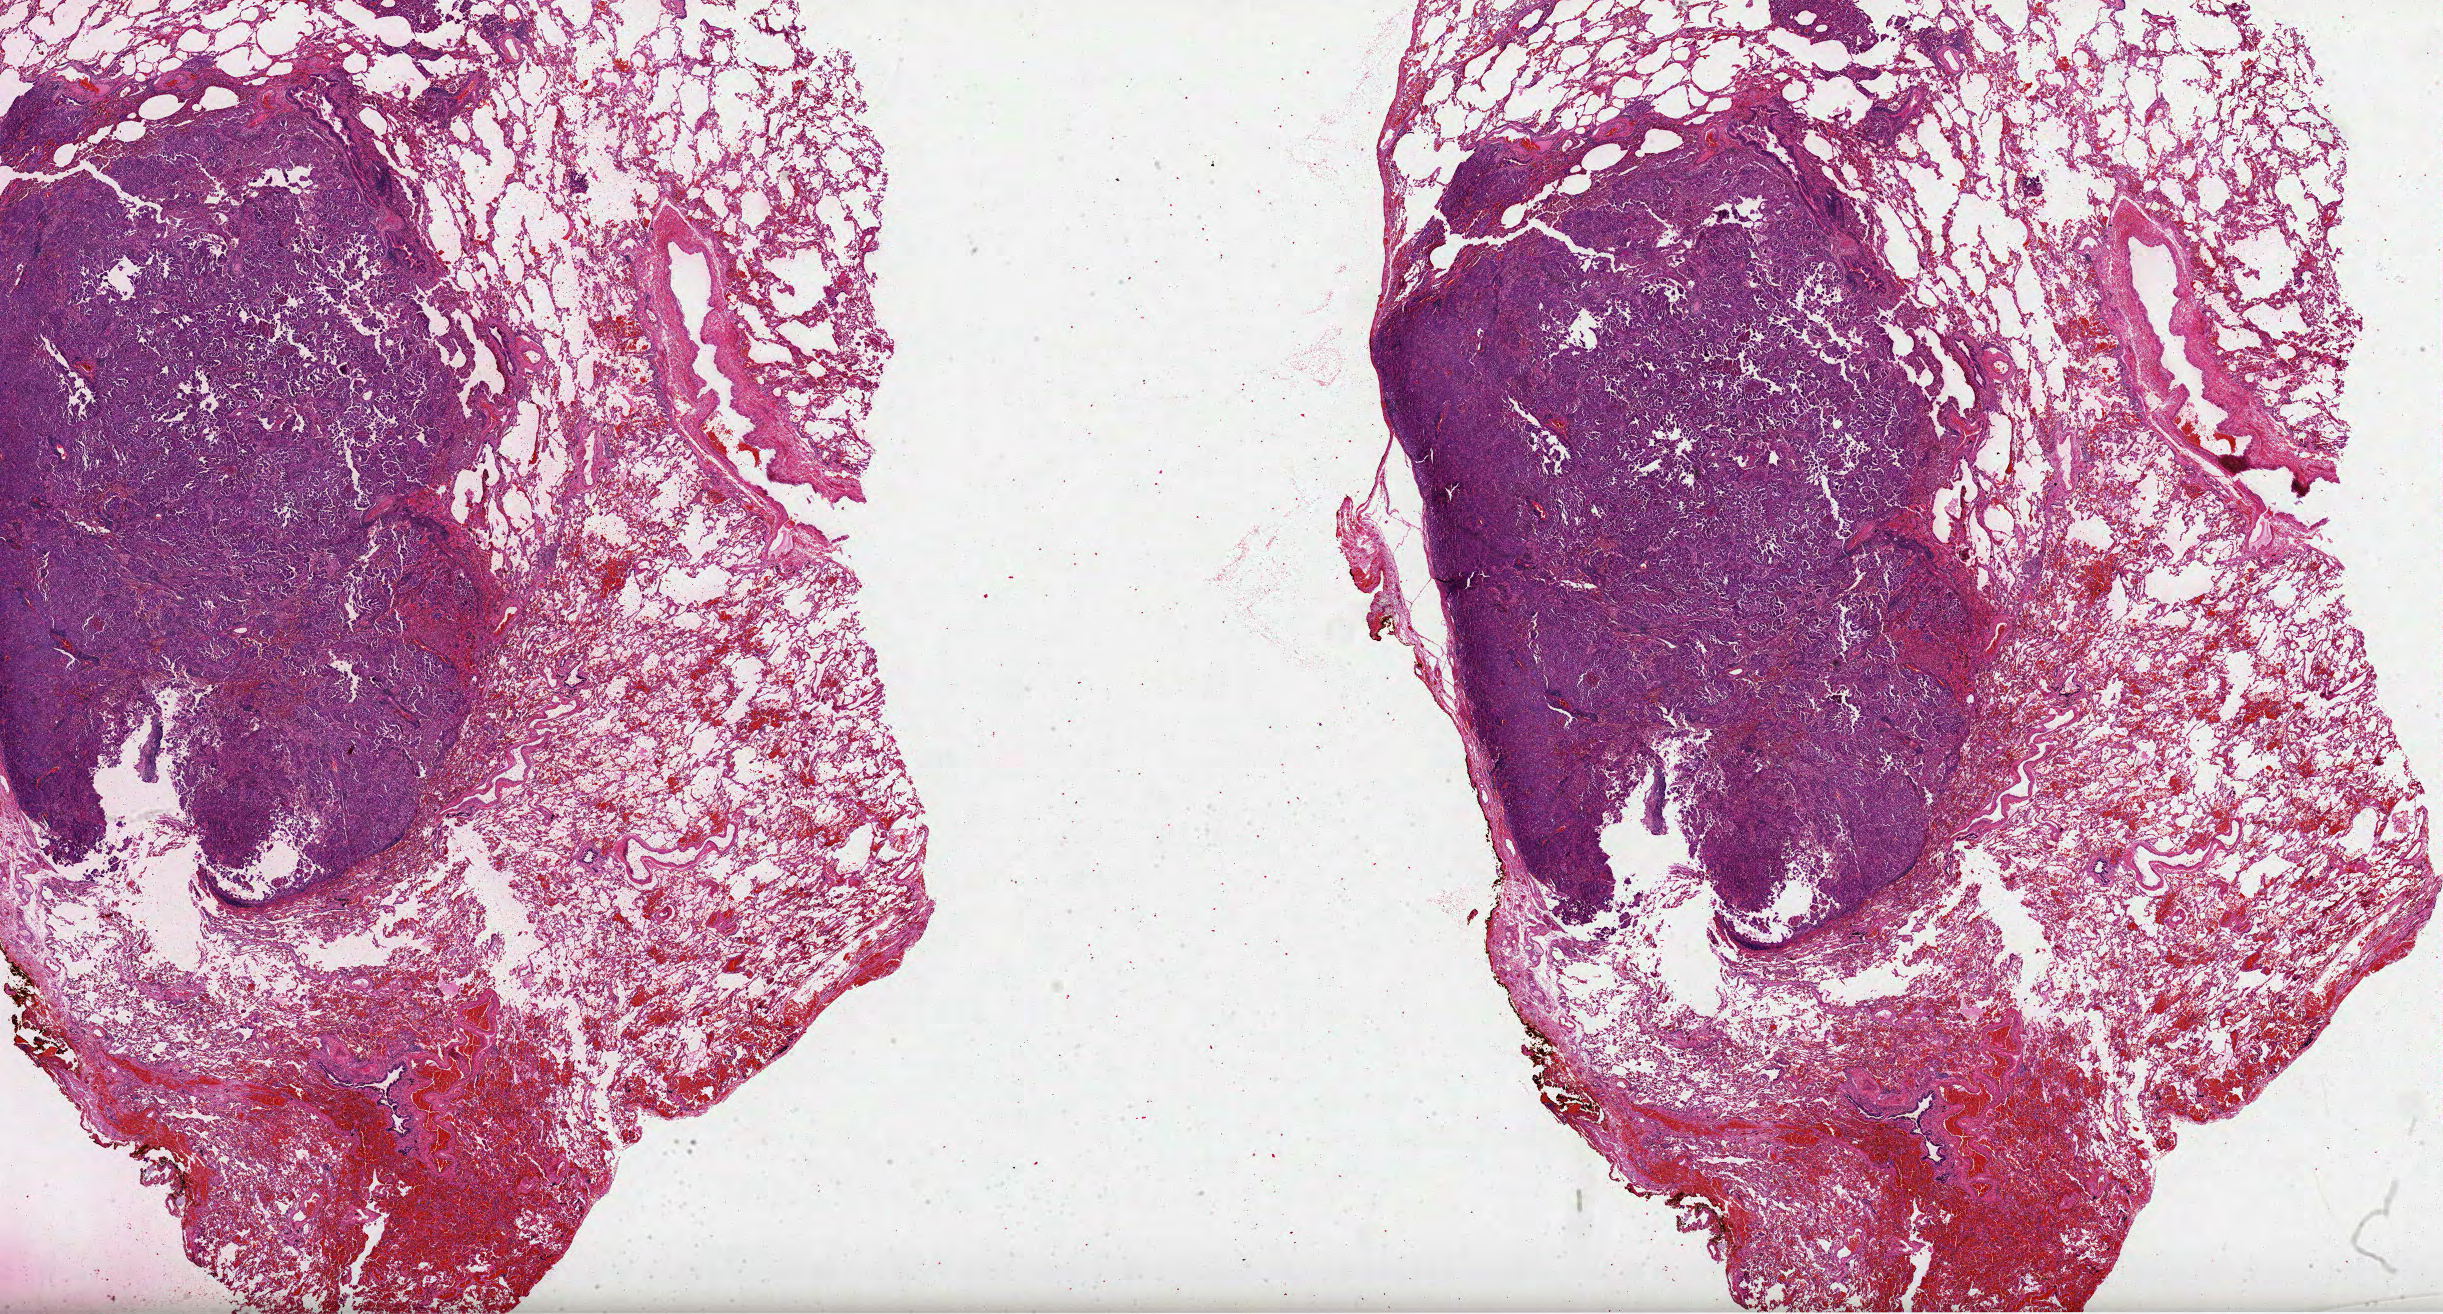
Whole-slide histology image, Hematoxylin and eosin (H&E) stained — whole scanned area (about 39.4 x 21.2 mm, from a 40x scan) shown as a low-resolution overview. FFPE section. Lung, primary tumour sample. Patient: male, age at initial diagnosis 82 years.
* AJCC pathologic stage: IIIA
* laterality: left
* diagnosis: Papillary adenocarcinoma, NOS
* TNM: T2a N2 M0